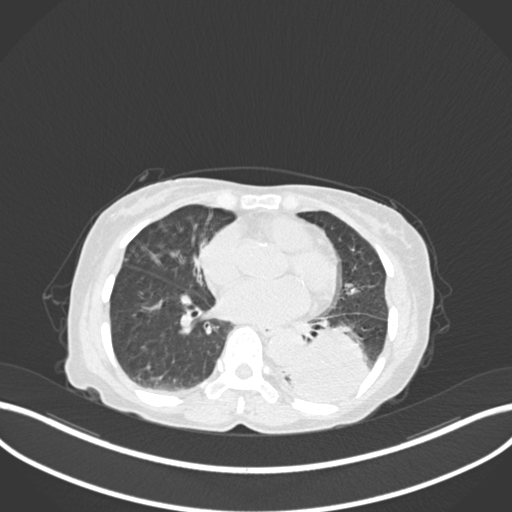
Chest CT, one axial slice. Position 59 of 233 along the scan axis. 120 kVp. Lung window (W 1500 / L -600 HU). 512 × 512 image matrix, field of view 400 × 400 mm. Female patient, age 78 years. From the clinical record (not read from this slice): clinical TNM (as recorded): T3 N0 M1.
Outlined on this slice (bounding box drawn by a radiologist):
- lung tumour (recorded histology: squamous cell carcinoma): bounding box (x1, y1, x2, y2) in pixels: (286, 326, 376, 404)